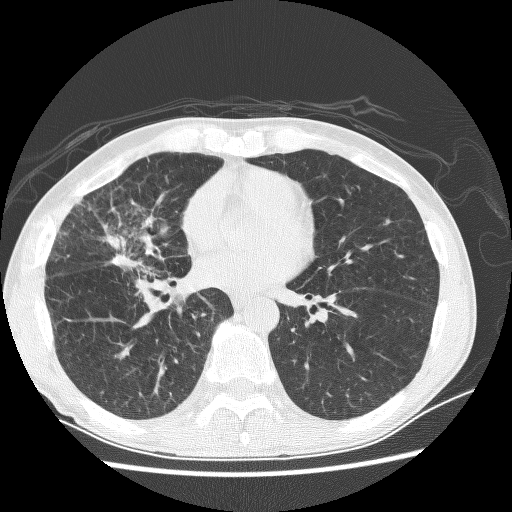
Low-dose screening chest CT, axial slice, first (baseline) screen, lung window (W 1500 / L -600 HU), lung (sharp) reconstruction kernel (BONE), 512 × 512 image matrix, field of view 340 × 340 mm. Male participant, aged 67 years at enrolment. Current smoker at enrolment.
Expert-annotated lung lesion, bounding box [x1, y1, x2, y2] px = [83, 213, 176, 283]. The exam's reader record, not a measurement of the box and not confirmed to be the same lesion: non-calcified nodule or mass ≥4 mm, right middle lobe, 28 × 18 mm, spiculated (stellate) margins, soft tissue attenuation. Participant outcome: lung cancer diagnosed 69 days after this screen — adenocarcinoma, NOS, right middle lobe, stage IV (AJCC 6th edition), 60 mm at pathology.